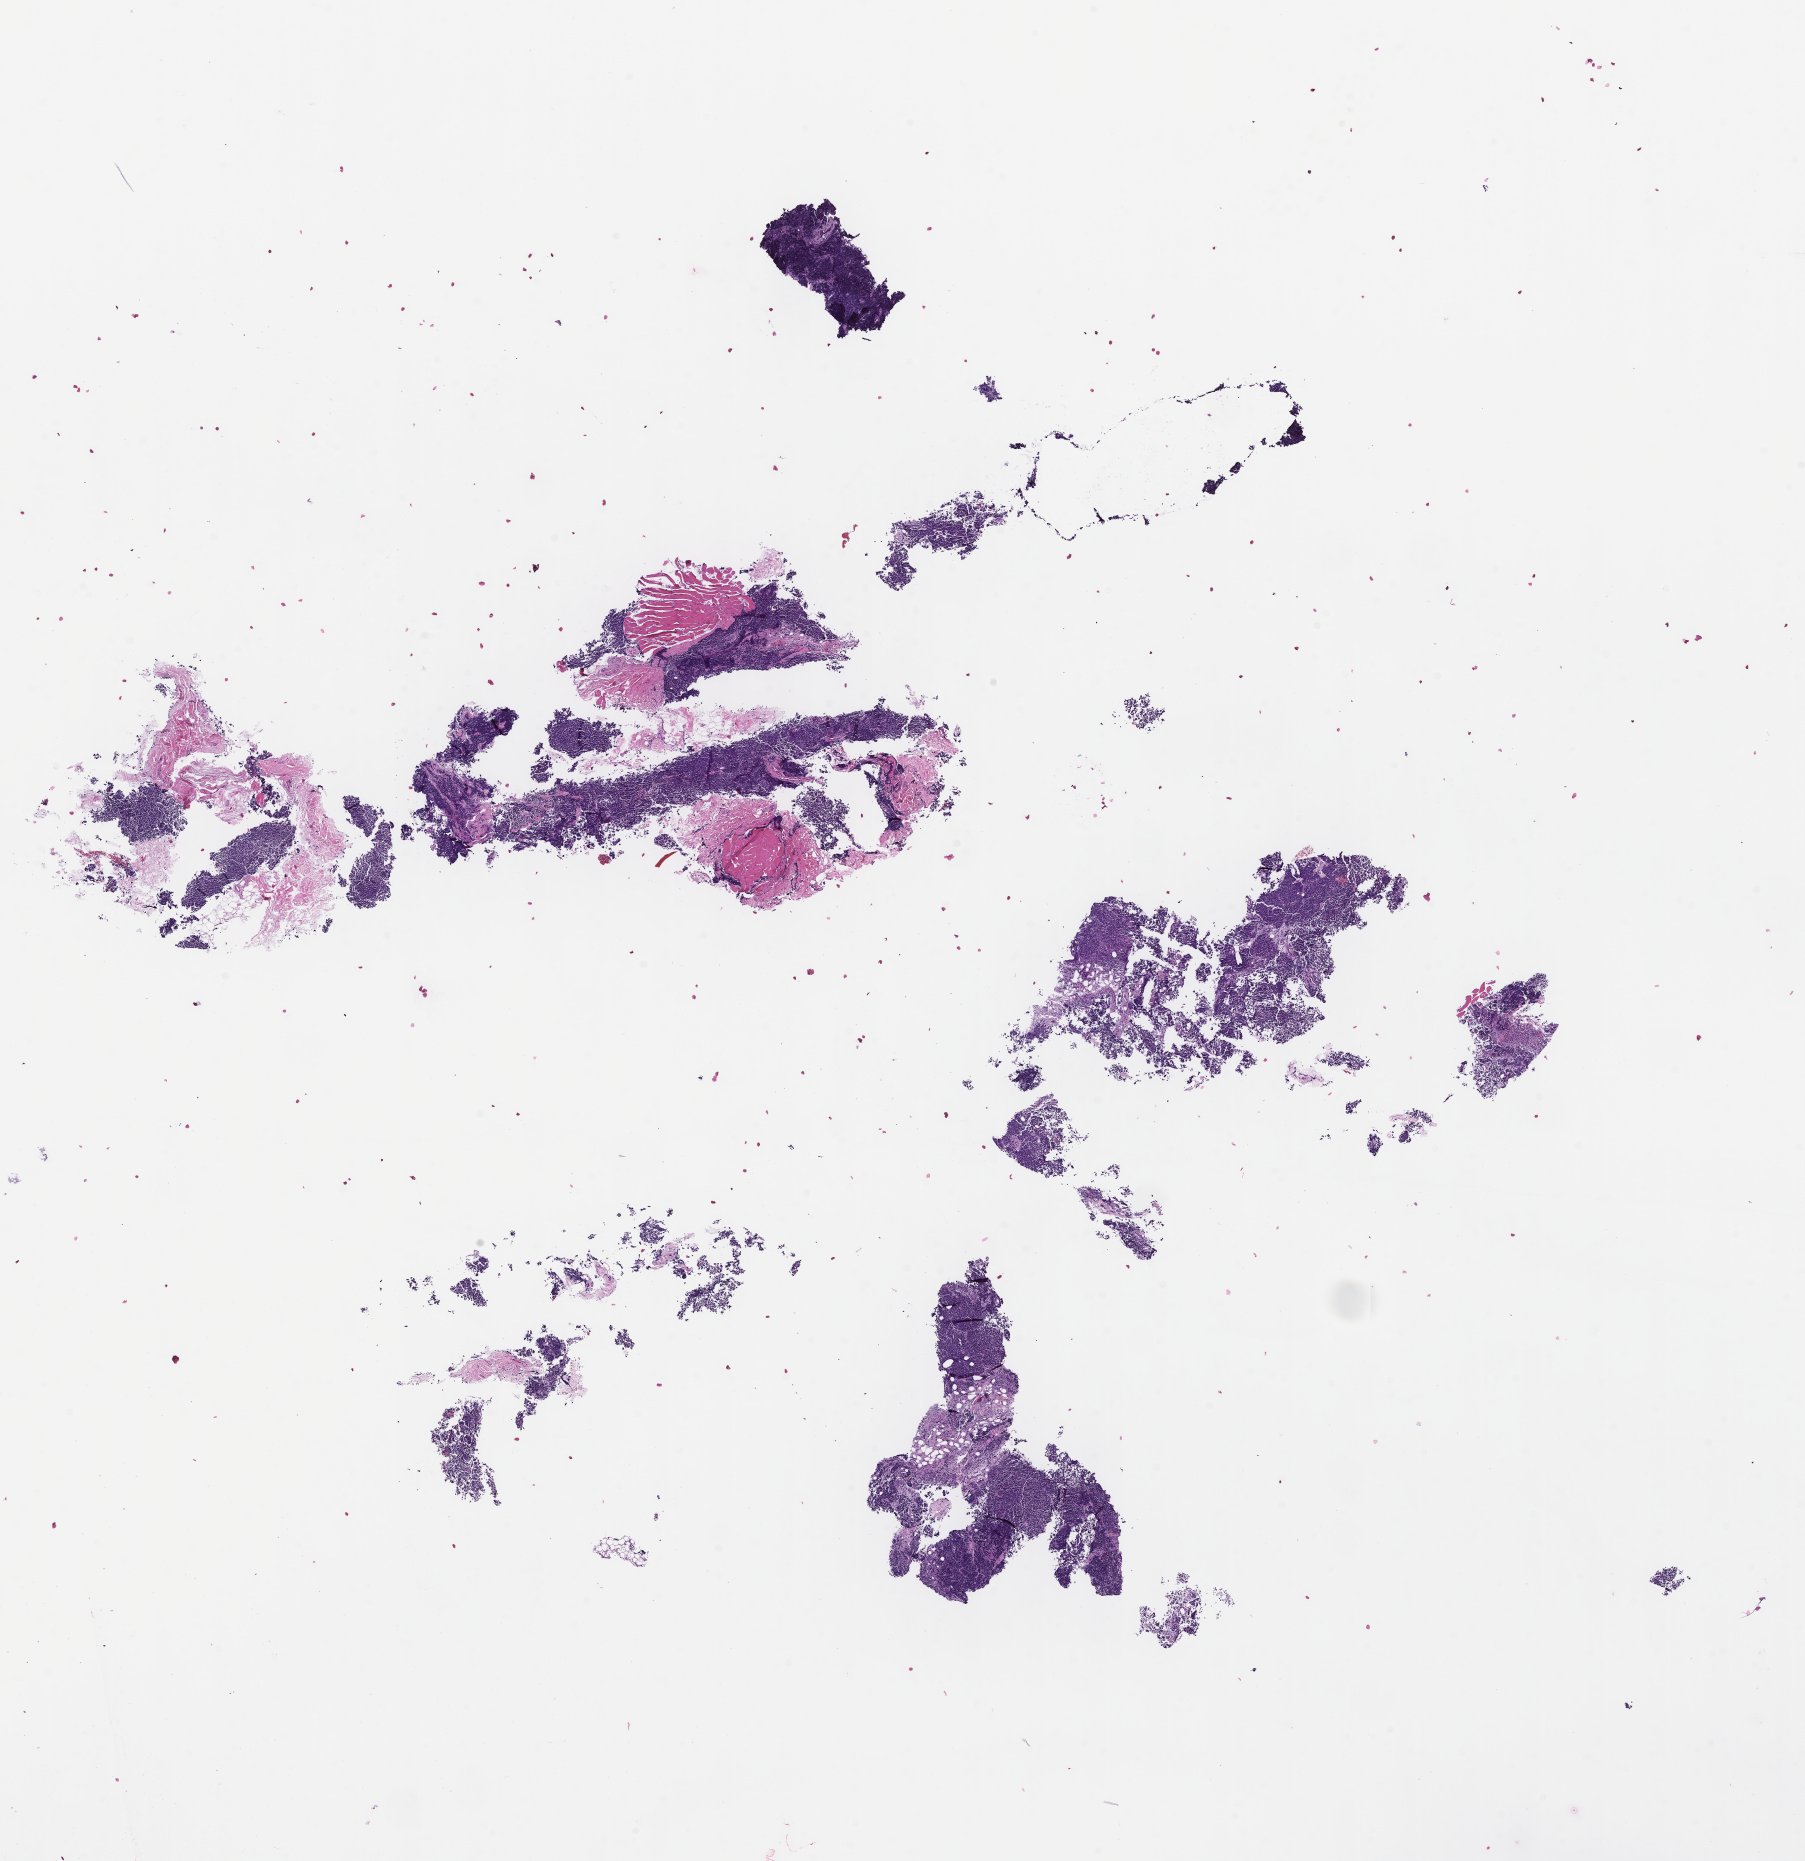
Hematoxylin and eosin (H&E) whole-slide image — a low-resolution overview of the entire scanned area, about 14.6 x 15.0 mm, FFPE section. Female patient.
• this section: metastasis (sampled organ not recorded)
• patient diagnosis (primary): Small Cell Lung Carcinoma